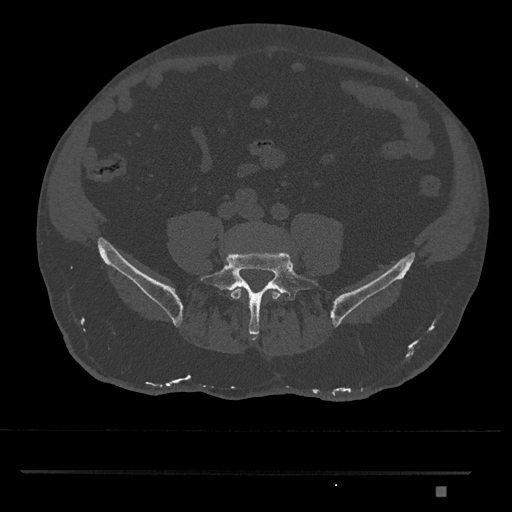
CT including the spine, one axial slice. Position 570 of 1134 along the scan axis. Reconstruction kernel Br40s/3. 120 kVp. Bone window (W 1800 / L 400 HU). 512 × 512 image matrix, field of view 429 × 429 mm. Male patient, age 65 years. From the clinical record (not read from this slice): primary cancer: prostate.
Structures marked on this image (semi-automatic segmentation, software-assisted and operator-edited):
- L4 vertebra: bounding box (x1, y1, x2, y2) in pixels: (230, 287, 282, 300)
- L5 vertebra: (200, 250, 321, 338)